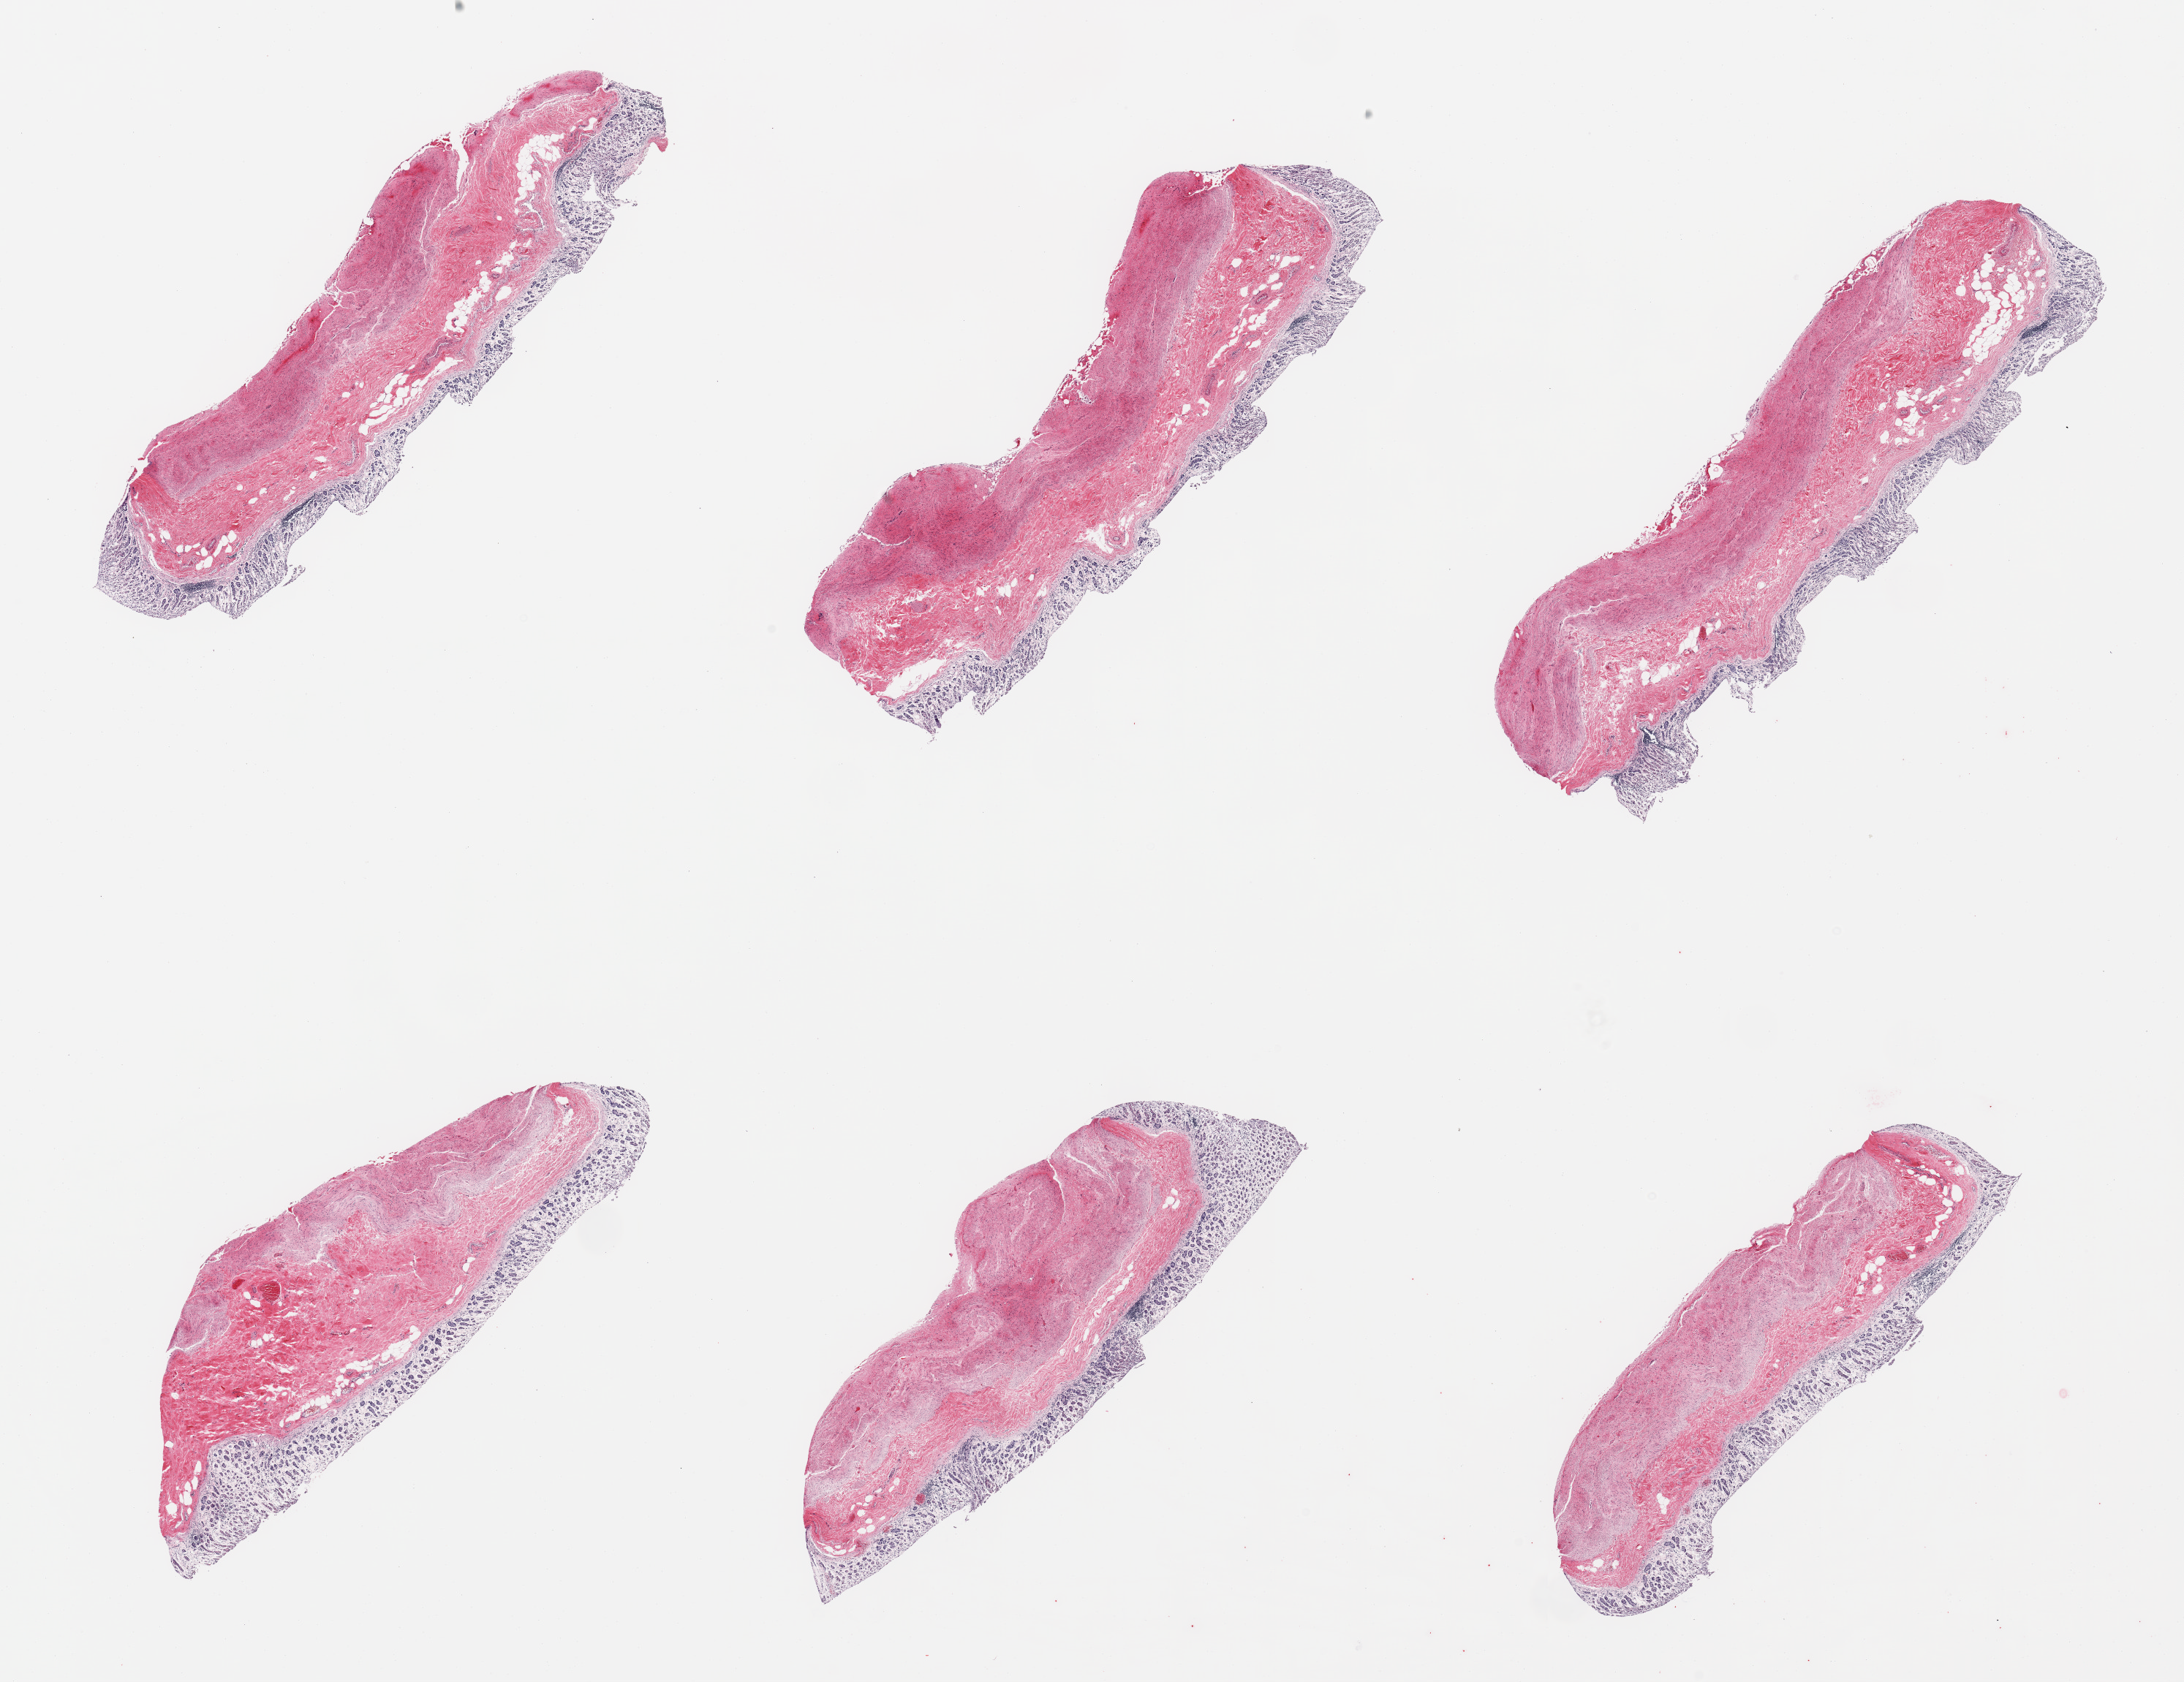
Whole-slide image, hematoxylin and eosin (H&E) stain, brightfield — low-resolution overview of the scanned area, about 23.6 x 18.2 mm (from a 20x scan). PAXgene-fixed, paraffin-embedded tissue. Section of stomach (target tissue). Tissue donor sample. Male donor.
Pathologist's review note for this sample: 6 pieces; autolyzed mucosa and muscularis propria.